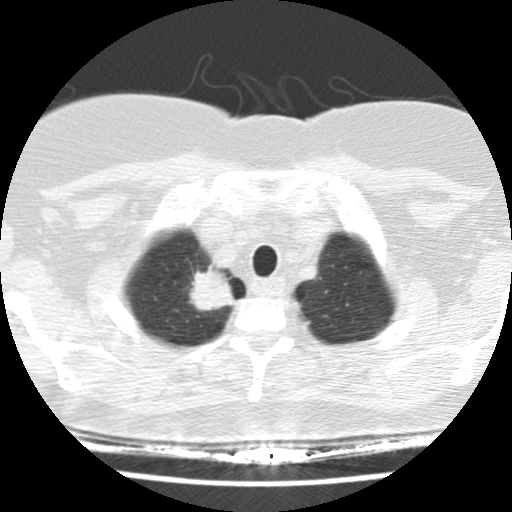
Low-dose screening chest CT, axial slice; baseline screening round; lung window (W 1500 / L -600 HU); 2.5 mm slice thickness; slice 16 of 148 in the series; 512 × 512 image matrix, field of view 281 × 281 mm. Female, age 58 years at enrolment. Former smoker at enrolment.
- Expert reader's lesion annotation, bounding box <168,253,246,330> (left, top, right, bottom; pixels).
- Screening reader's record for this exam (one nodule recorded; not confirmed to be the boxed lesion): non-calcified nodule or mass ≥4 mm, right upper lobe, 28 × 24 mm, spiculated (stellate) margins, soft tissue attenuation.
- Lung cancer was diagnosed 40 days after this screen: adenocarcinoma, NOS, right upper lobe, poorly differentiated (G3), stage IB (AJCC 6th edition), 29 mm at pathology.